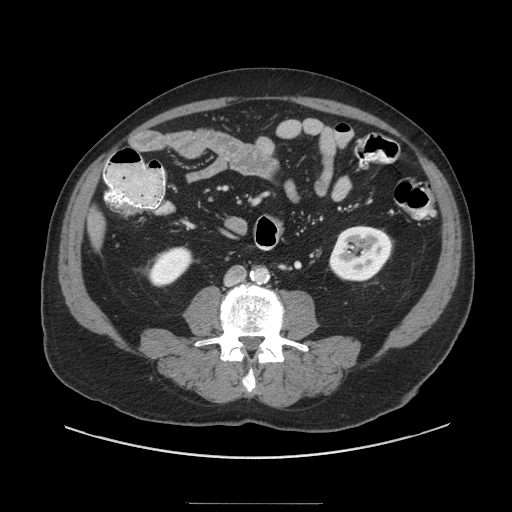
Contrast-enhanced abdominal CT (liver protocol), one axial slice. Position 14 of 91 along the scan axis. 140 kVp. Soft-tissue window (W 400 / L 40 HU). 2.5 mm slice thickness. 512 × 512 image matrix, field of view 440 × 440 mm. Case-level facts recorded for this patient, not image findings: diagnosis: hepatocellular carcinoma (patient treated with transarterial chemoembolisation; whether this scan precedes or follows treatment is not stated here); TNM stage (as recorded): Stage-I; Child-Pugh class: A; tumour differentiation: well differentiated; tumour nodularity: uninodular.
Annotated regions visible in this slice (semi-automatic segmentation, software-assisted and operator-edited):
- liver parenchyma outside the tumour (the mass and vessels are separate outlines, so this box may not span the whole liver): bounding box (x1, y1, x2, y2) in pixels: (88, 210, 104, 246)